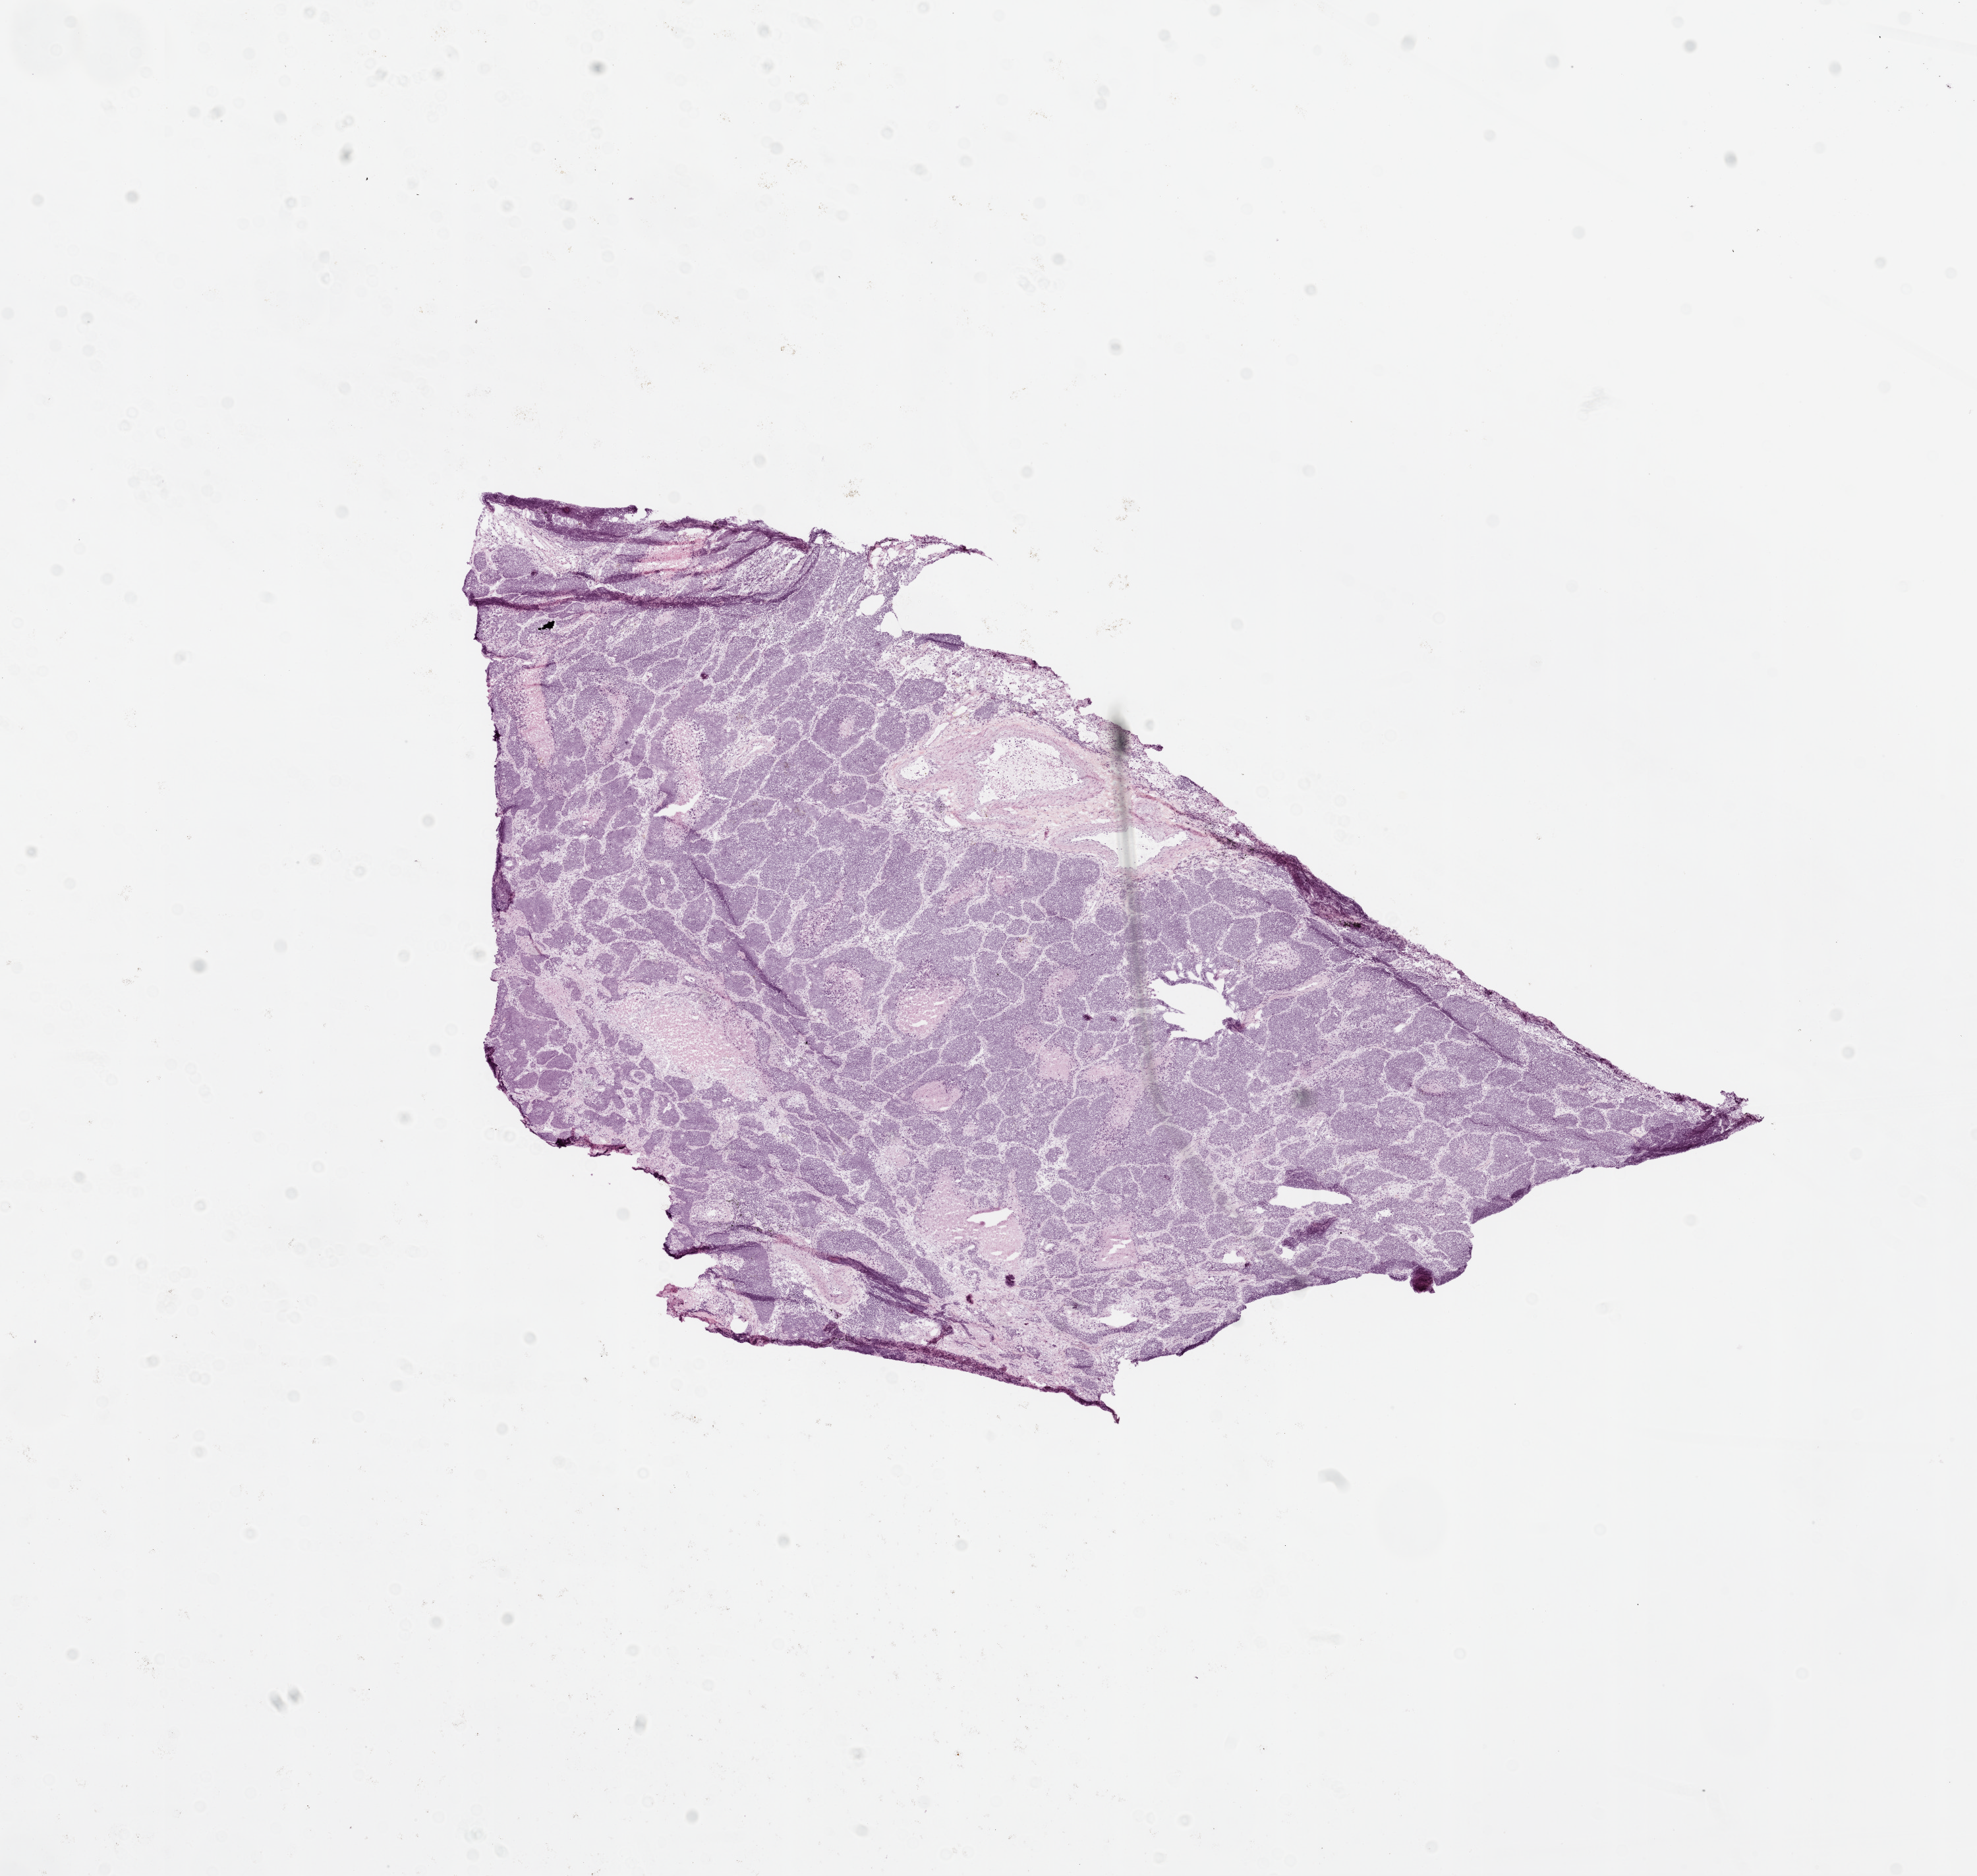
Whole-slide histology image, Hematoxylin and eosin (H&E) stained — shown as a low-resolution overview of the whole scanned area (about 12.0 x 11.4 mm, acquisition: 20x scan); frozen section; lung, primary tumour sample. Patient: female, age at initial diagnosis 74 years. Composition of this section per pathologist review: tumour cells 80%, tumour nuclei 90%.
Pathologic diagnosis: Basaloid squamous cell carcinoma.